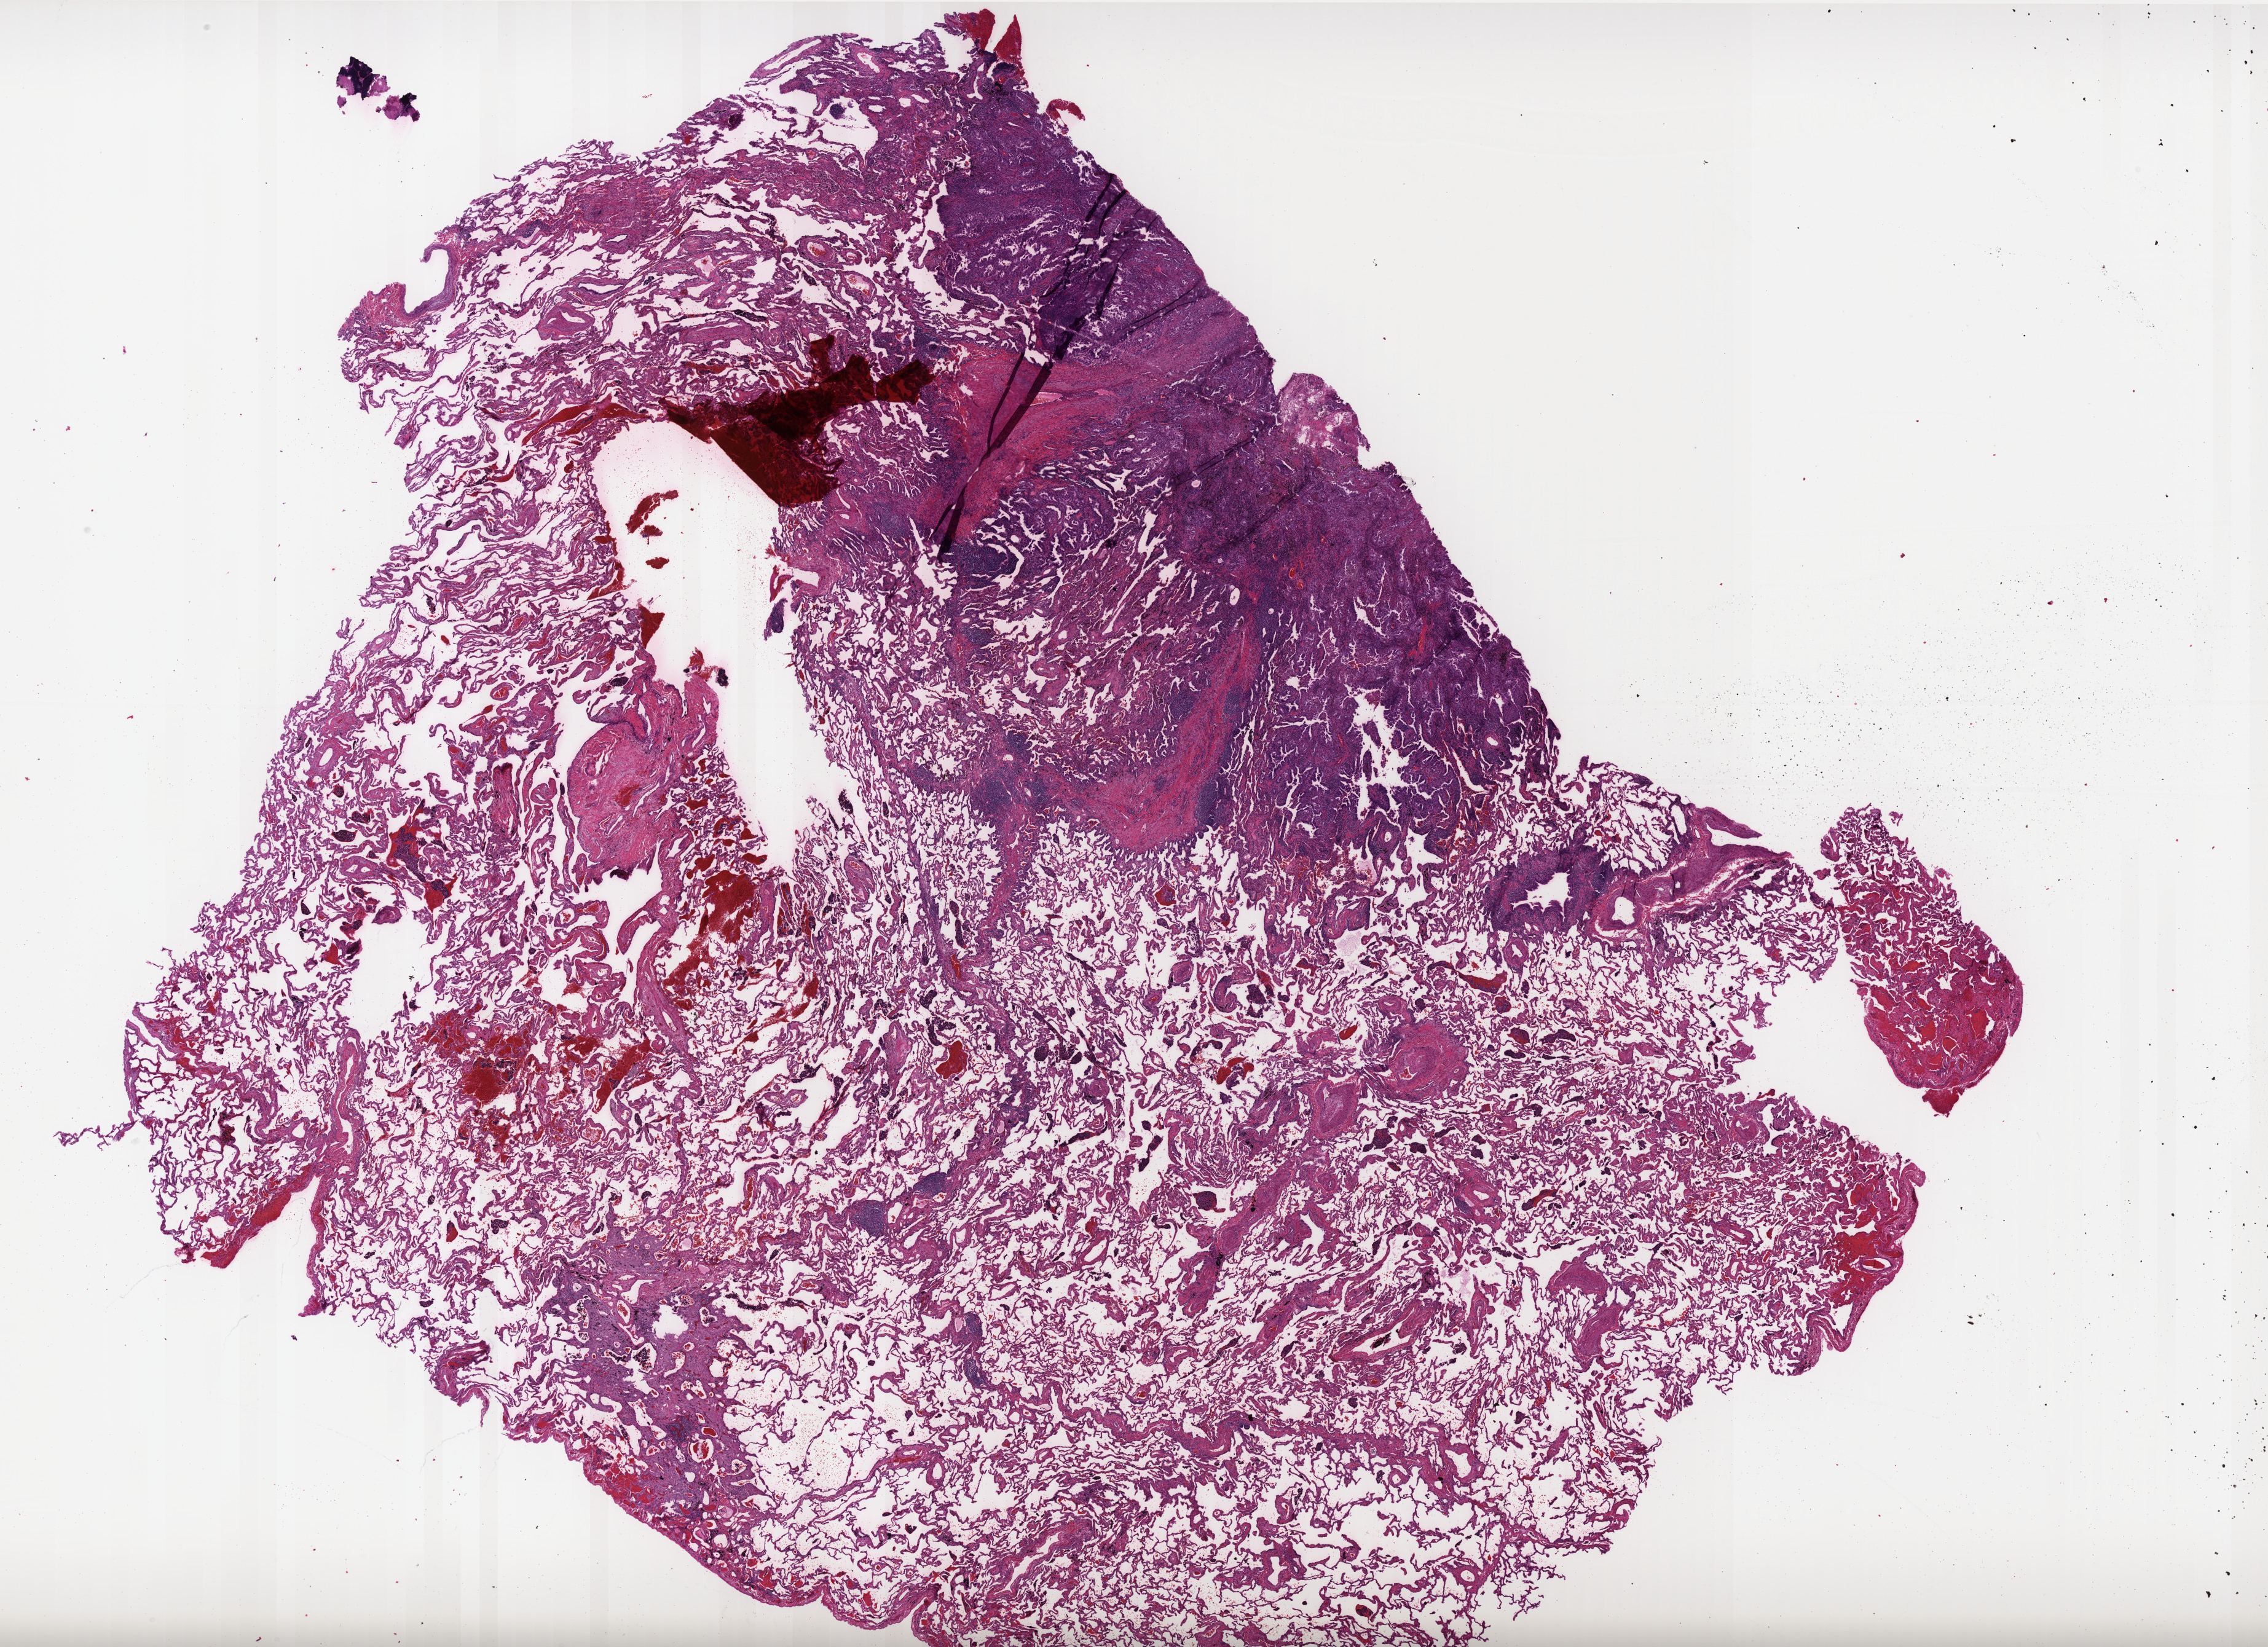
Digitized H&E tissue section (whole slide) — shown as a low-resolution overview of the whole scanned area (about 29.6 x 21.5 mm, slide scanned at 40x); formalin-fixed paraffin-embedded (FFPE) diagnostic section; sample: primary tumour, lung. Female, age 72 years at initial diagnosis.
- TNM: T1 N0 M0
- AJCC pathologic stage: IA (3rd edition)
- diagnosis: Adenocarcinoma, NOS
- laterality: left